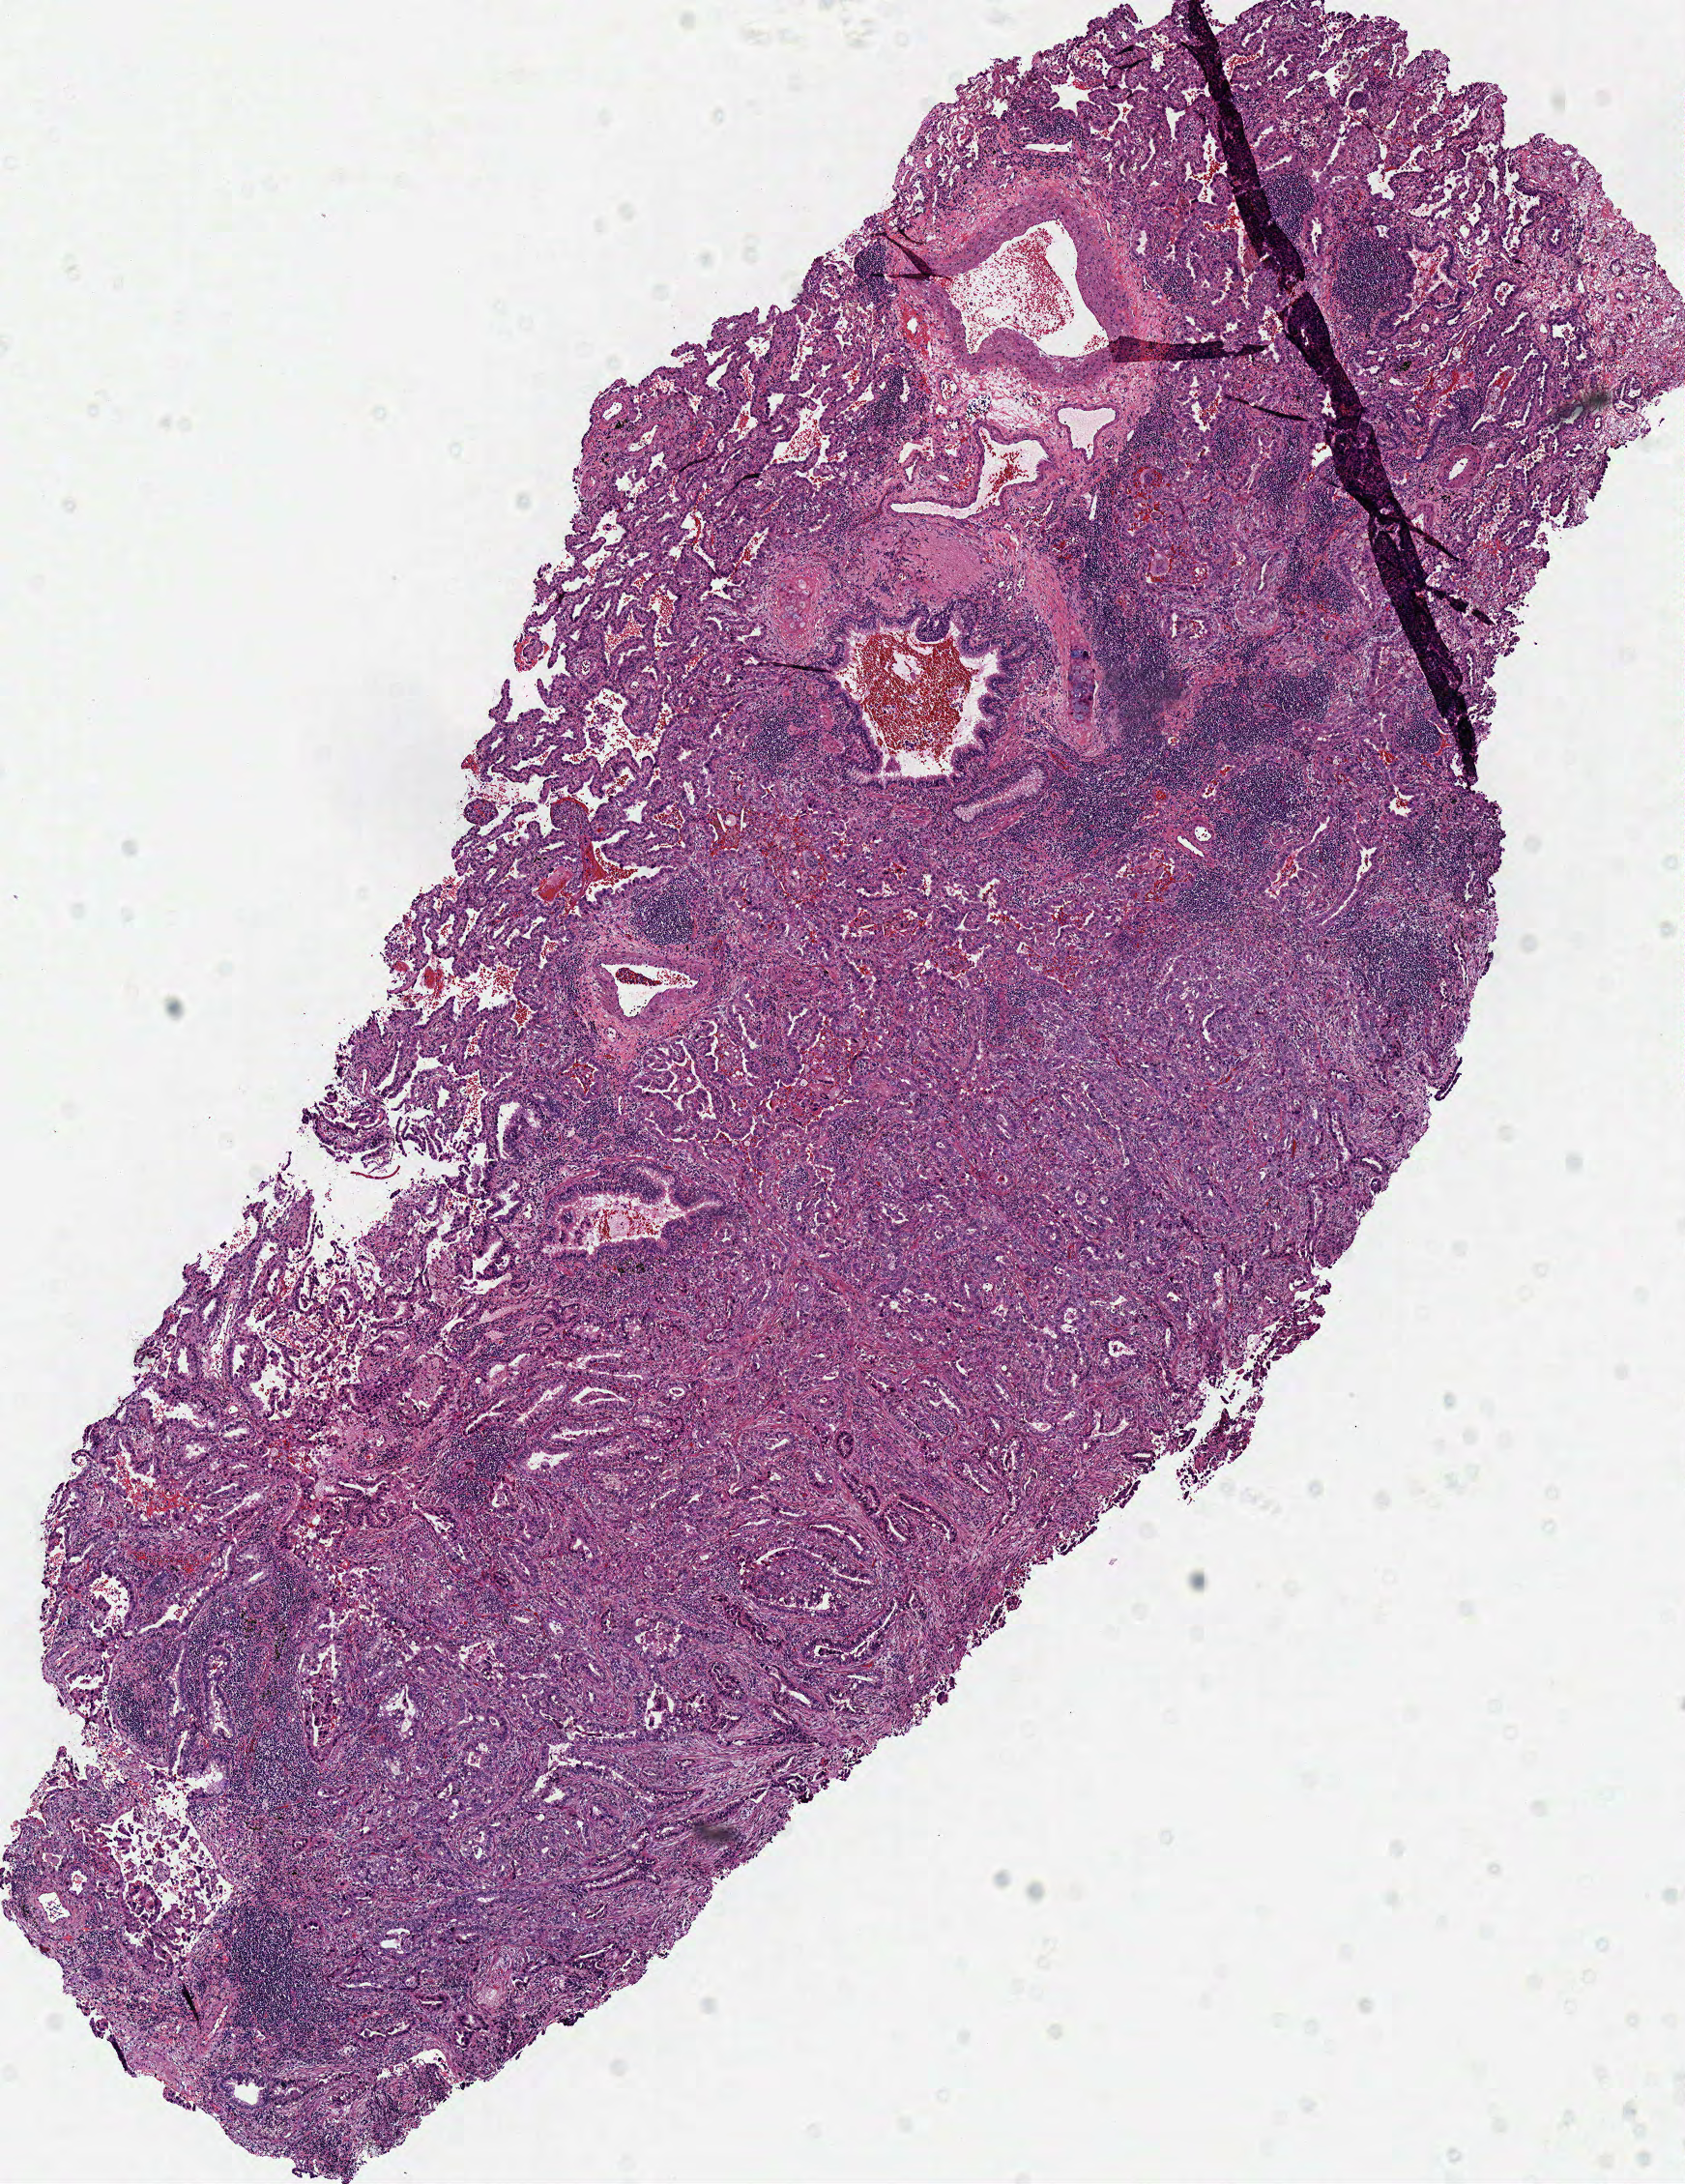
Whole-slide histology image, H&E-stained — a low-resolution overview of the entire scanned area, about 6.9 x 8.9 mm (acquisition: 40x scan); frozen section from the top of the tissue portion; sample: primary tumour, lung. Patient: female, age at initial diagnosis 72 years. Composition of this section per pathologist review: tumour cells 100%, tumour nuclei 70%, normal cells 0%, stromal cells 0%, necrosis 0%. Inflammatory infiltration, as recorded: lymphocyte infiltration 20%, monocyte infiltration 1%, neutrophil infiltration 0%.
* diagnosis: Adenocarcinoma, NOS (upper lobe, lung)
* TNM: T2a N0 MX
* laterality: right
* AJCC pathologic stage: IB (7th edition)